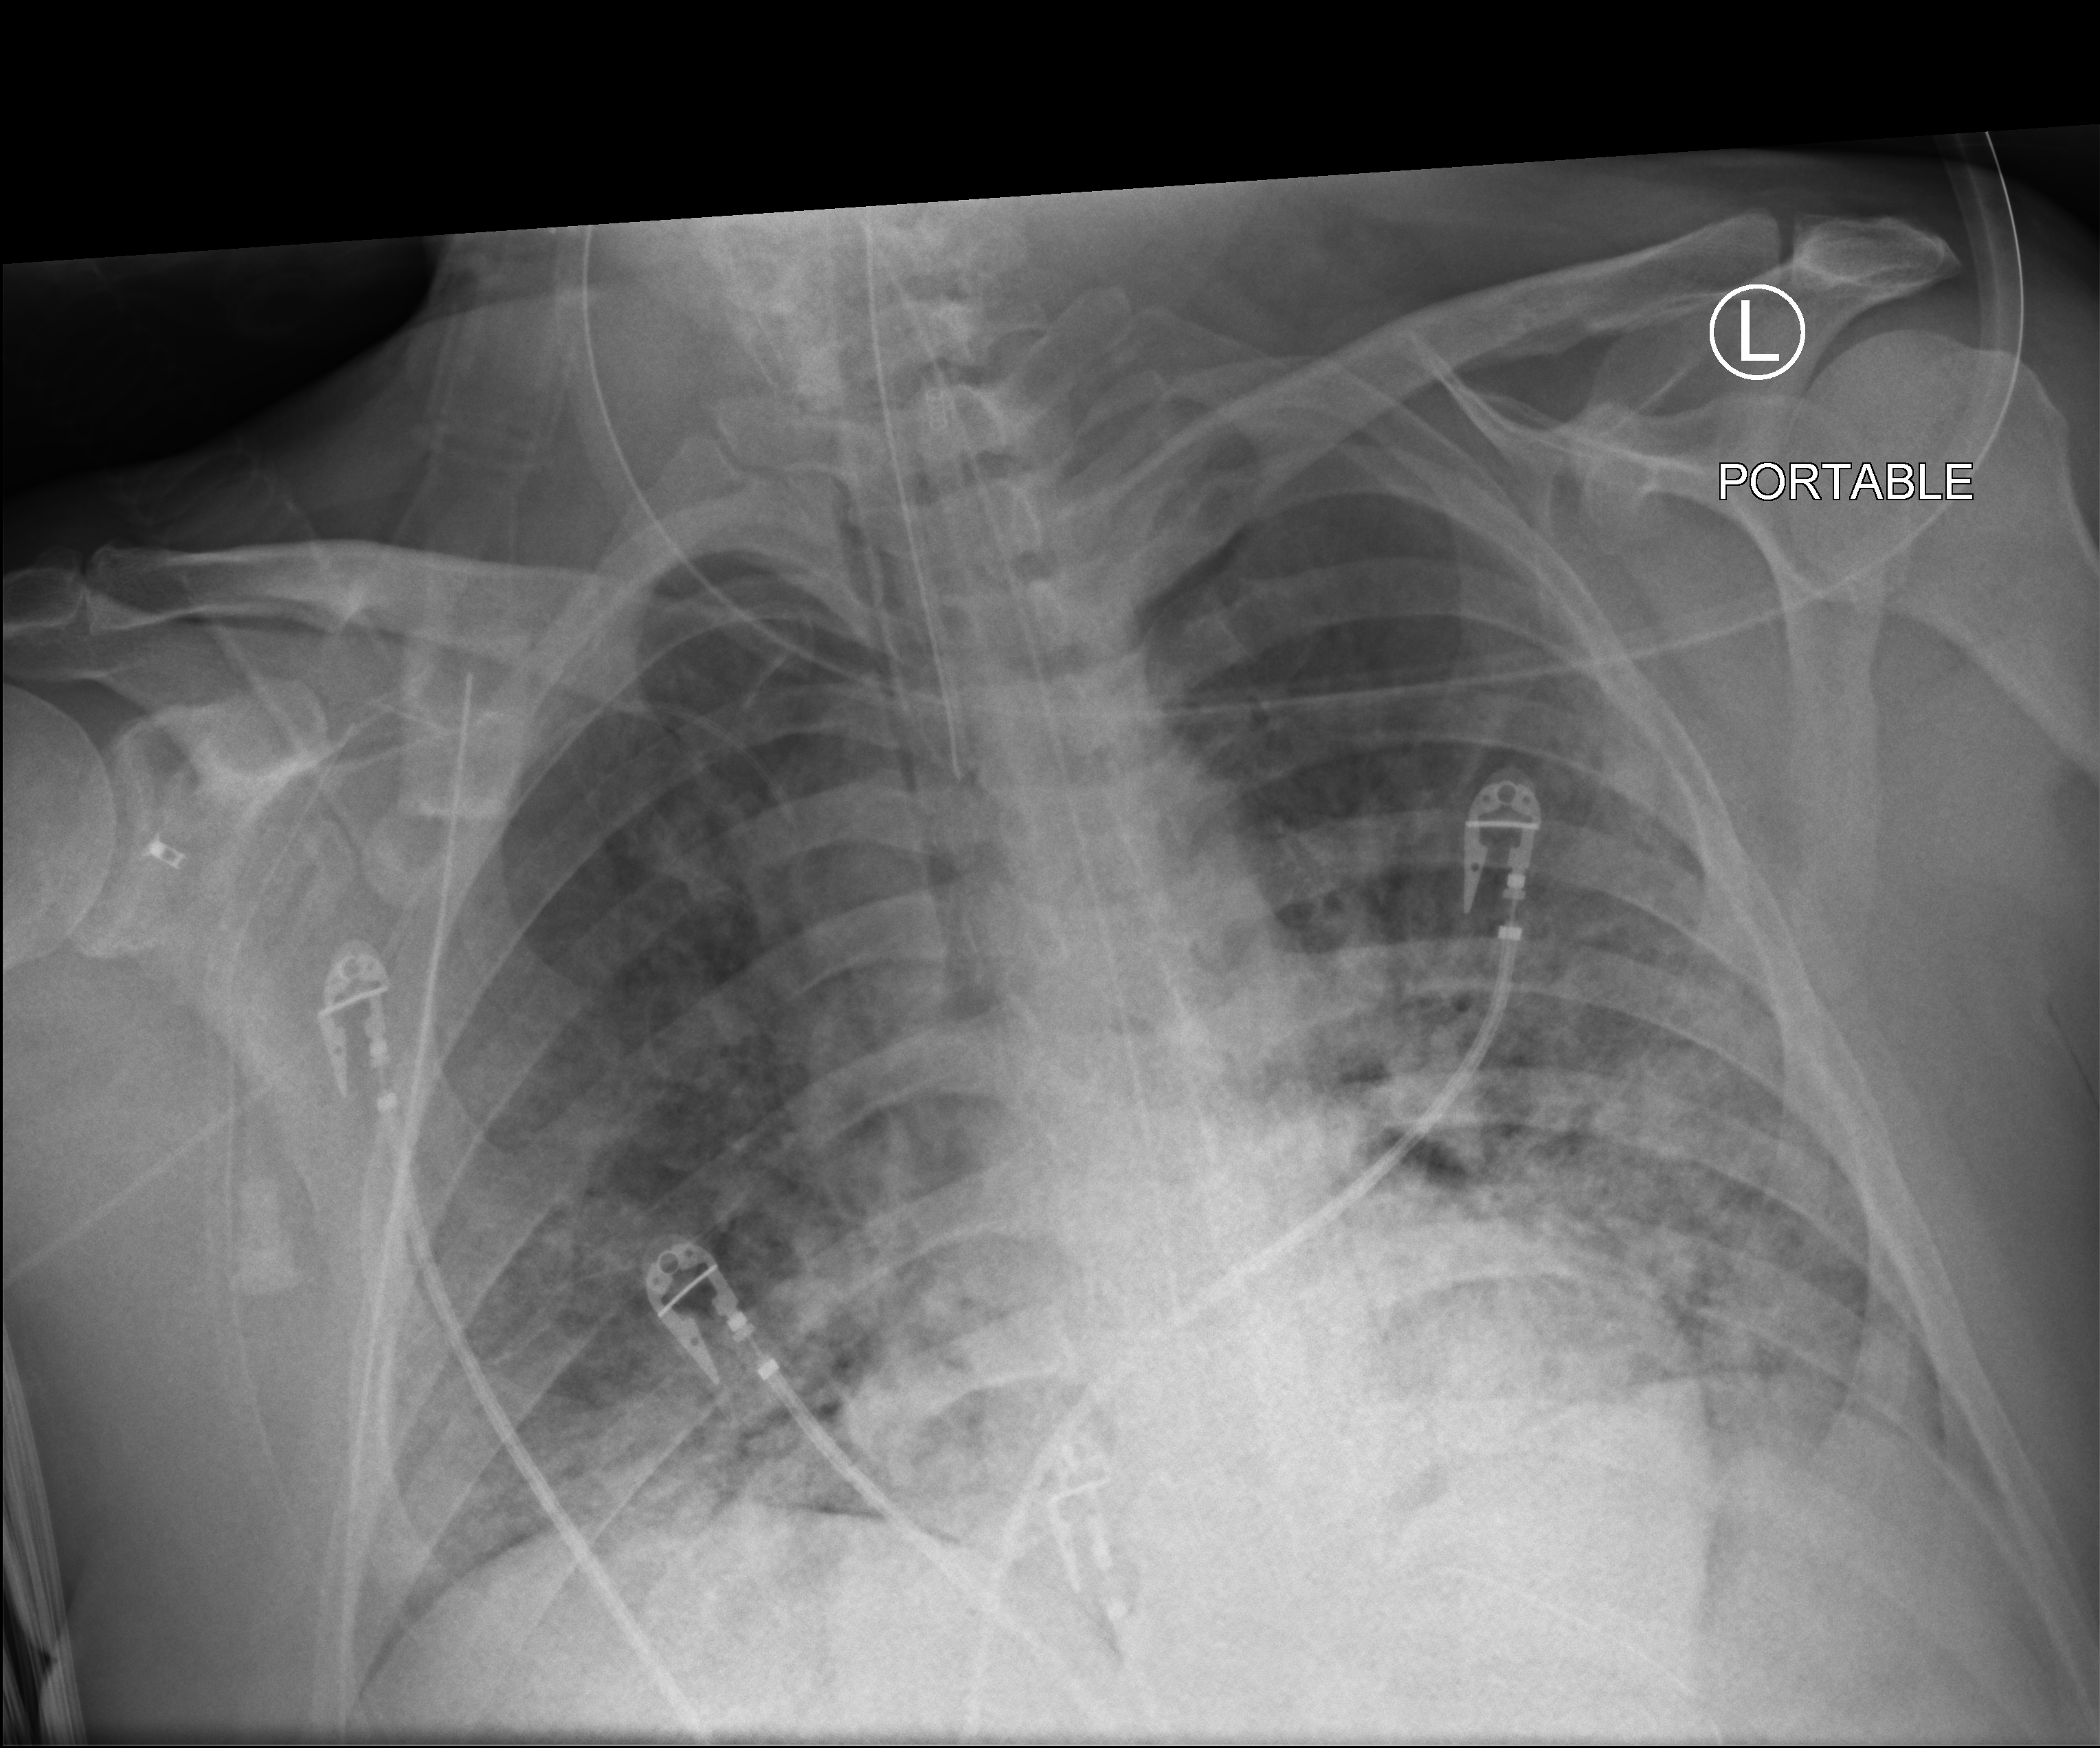
Portable chest radiograph. Male patient hospitalised with COVID-19, age 18–59 years.
Admission-level facts for this patient (not findings on this image; timing relative to this image not recorded): mechanically ventilated during this hospital stay: yes; hypertension (admission record): no; COPD (admission record): no.